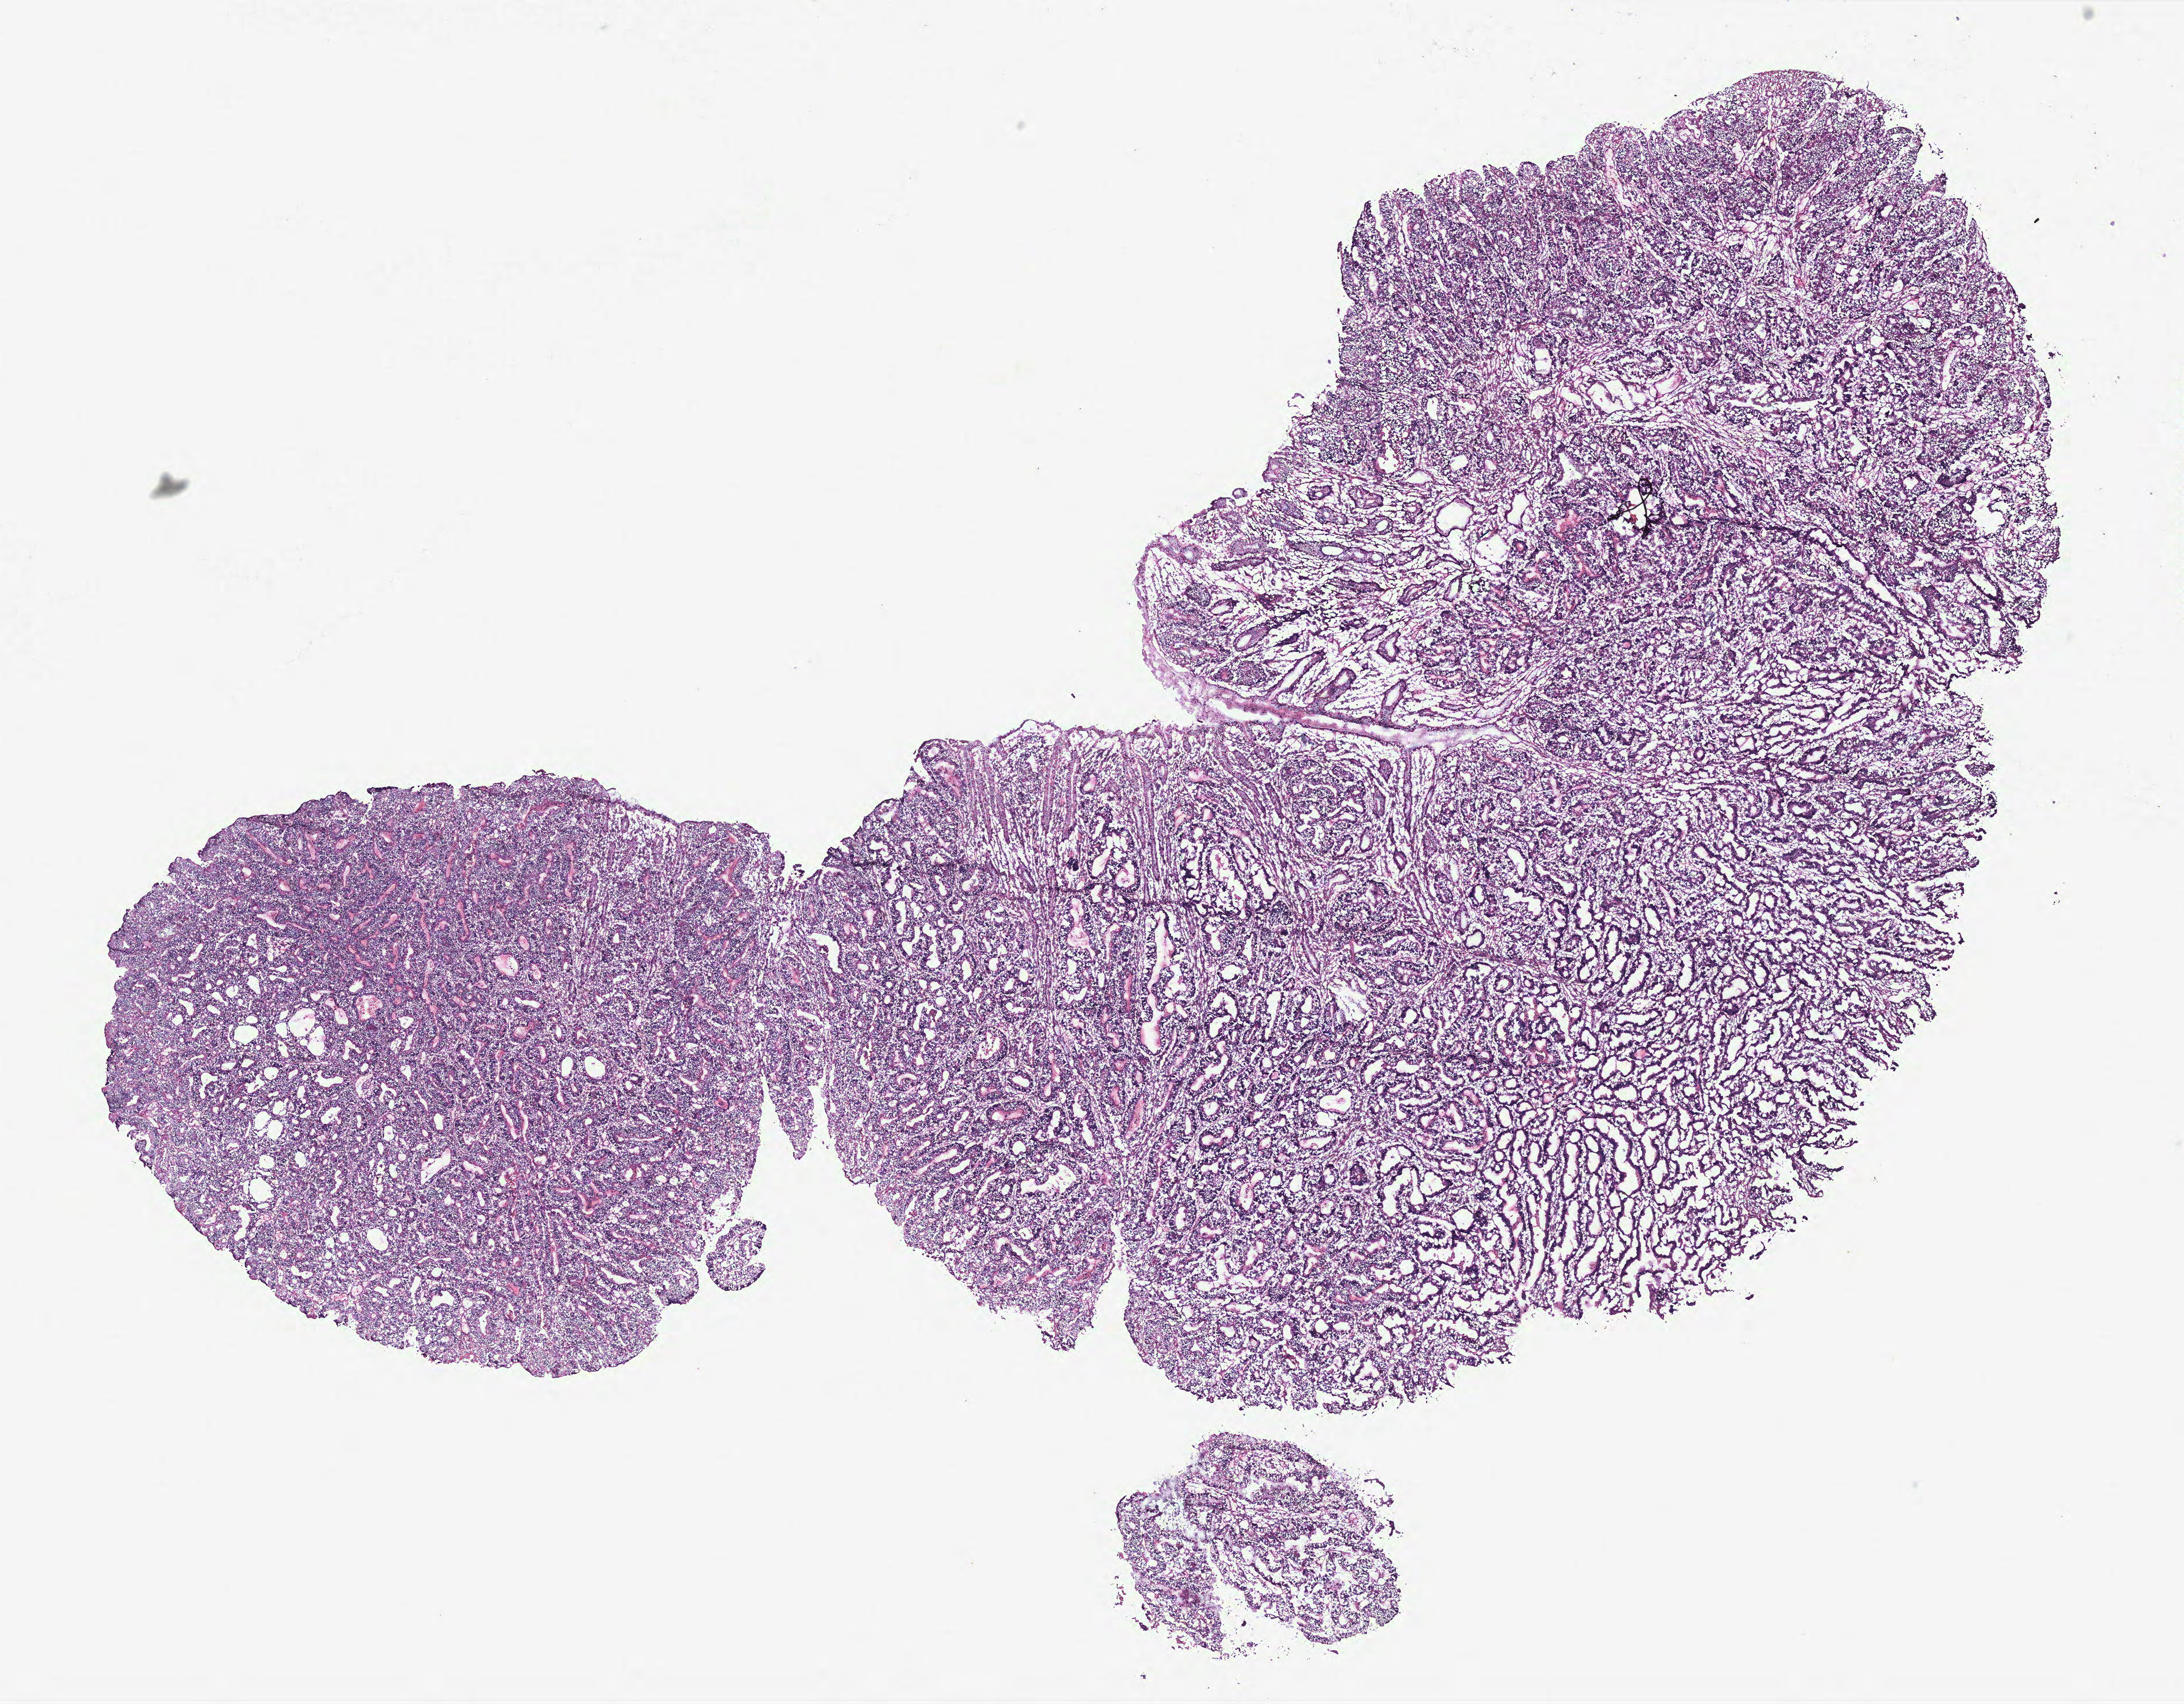
Digitized H&E tissue section (whole slide) — a low-resolution overview of the entire scanned area, about 15.1 x 11.8 mm (acquisition: 40x scan); colon, tissue type not recorded.
• patient diagnosis (cohort enrolment): colon cancer (colon)